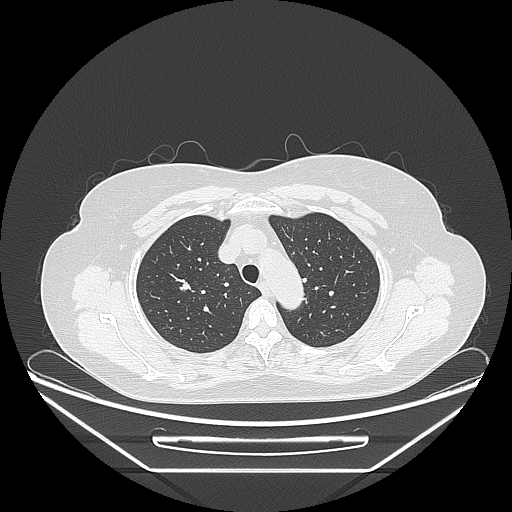
Chest CT, one axial slice; slice 192 of 236 in the series (ordered by position); reconstruction kernel LUNG; lung window (W 1500 / L -600 HU); 512 × 512 image matrix. Female patient, age 60 years. From the clinical record (not read from this slice): clinical TNM (as recorded): T1c N0 M0; histopathological grade: G2-3.
Annotated regions visible in this slice (rectangle marked by the reading radiologist):
- lung tumour (recorded histology: adenocarcinoma): bounding box <175,277,196,300> (left, top, right, bottom; pixels)